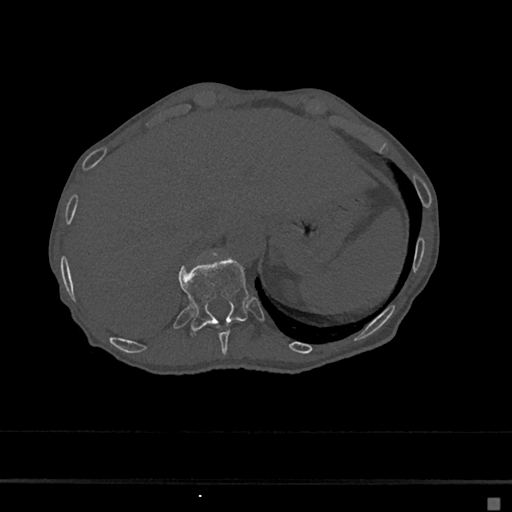
CT including the spine, one axial slice; slice 186 of 797 in the series (ordered by position); reconstruction kernel Br40s/3; 120 kVp; bone window (W 1800 / L 400 HU); 0.5 mm slice thickness; 512 × 512 image matrix, field of view 360 × 360 mm. Female patient, age 68 years. From the clinical record (not read from this slice): primary cancer: renal.
Outlined on this slice (semi-automatically segmented with operator editing):
- T10 vertebra: bounding box [x1, y1, x2, y2] px = [216, 321, 239, 354]
- T11 vertebra: [179, 258, 249, 330]